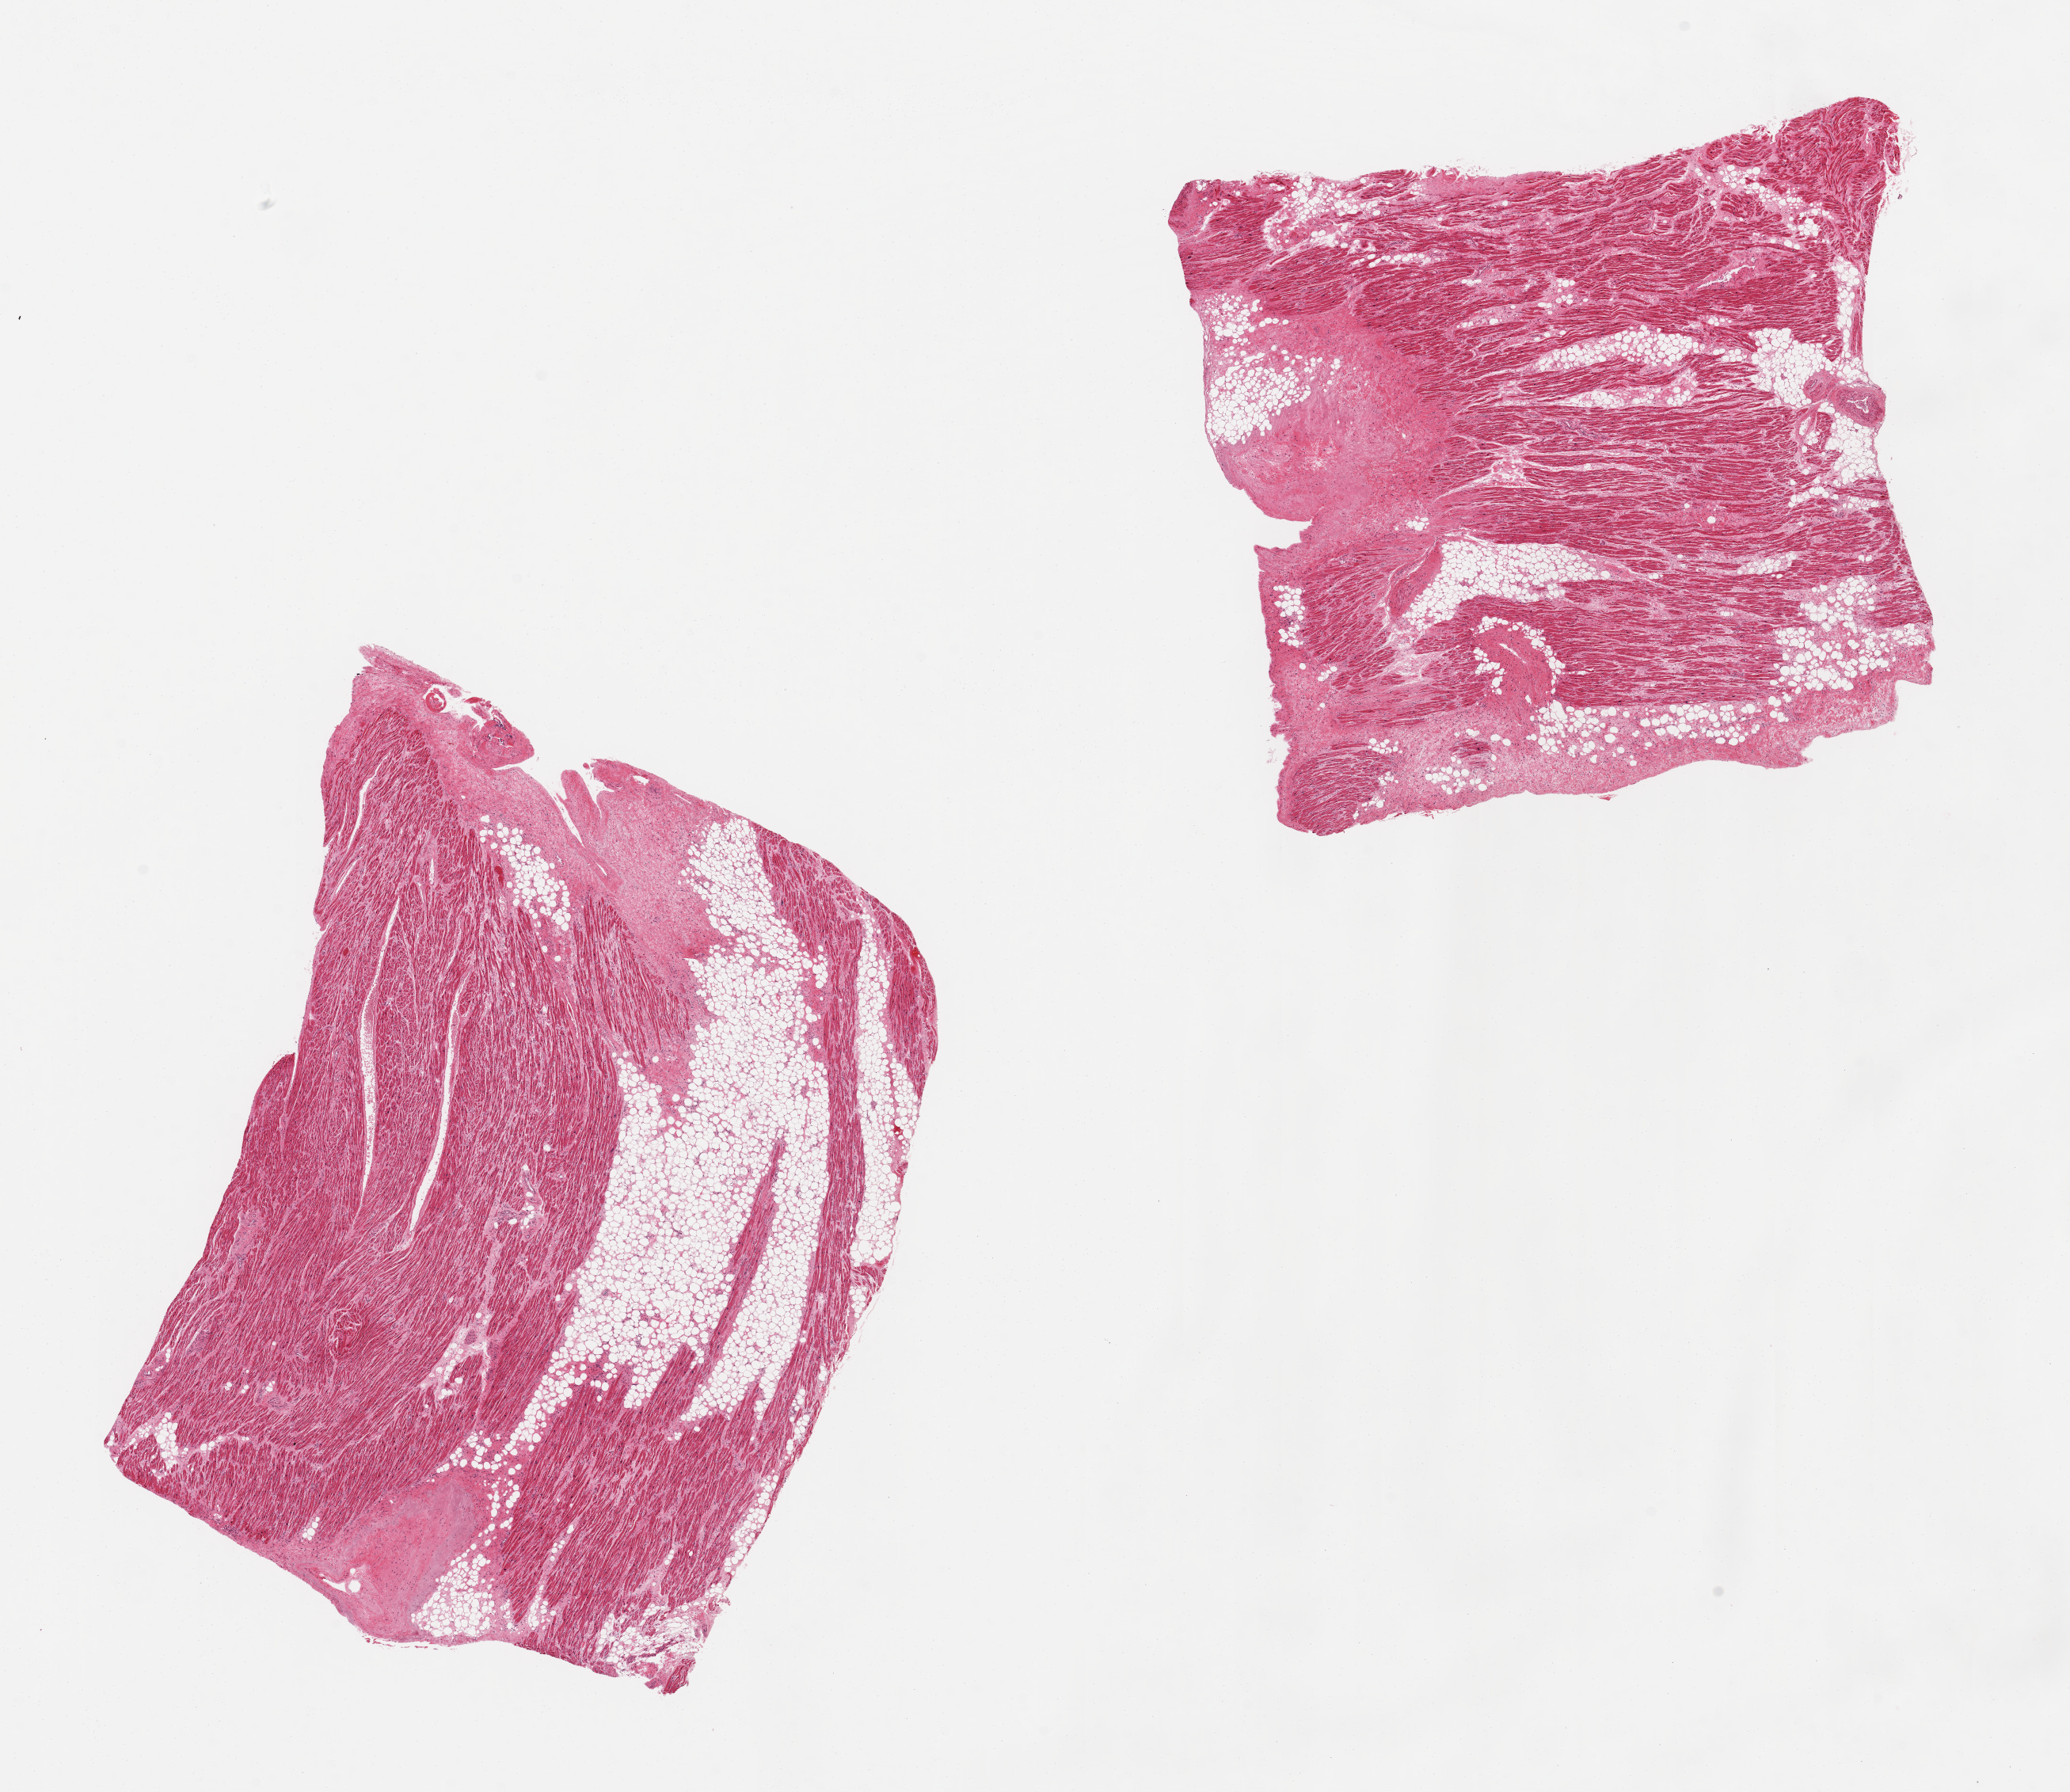
Whole-slide image, haematoxylin and eosin stain, shown as a low-resolution overview of the whole scanned area (about 20.7 x 17.9 mm, slide scanned at 20x), PAXgene-fixed paraffin-embedded (PFPE) section, target tissue: auricular appendage, tissue donor sample. Donor sex: male.
Reviewer comment on this tissue sample: 2 pieces, ~30% fat.